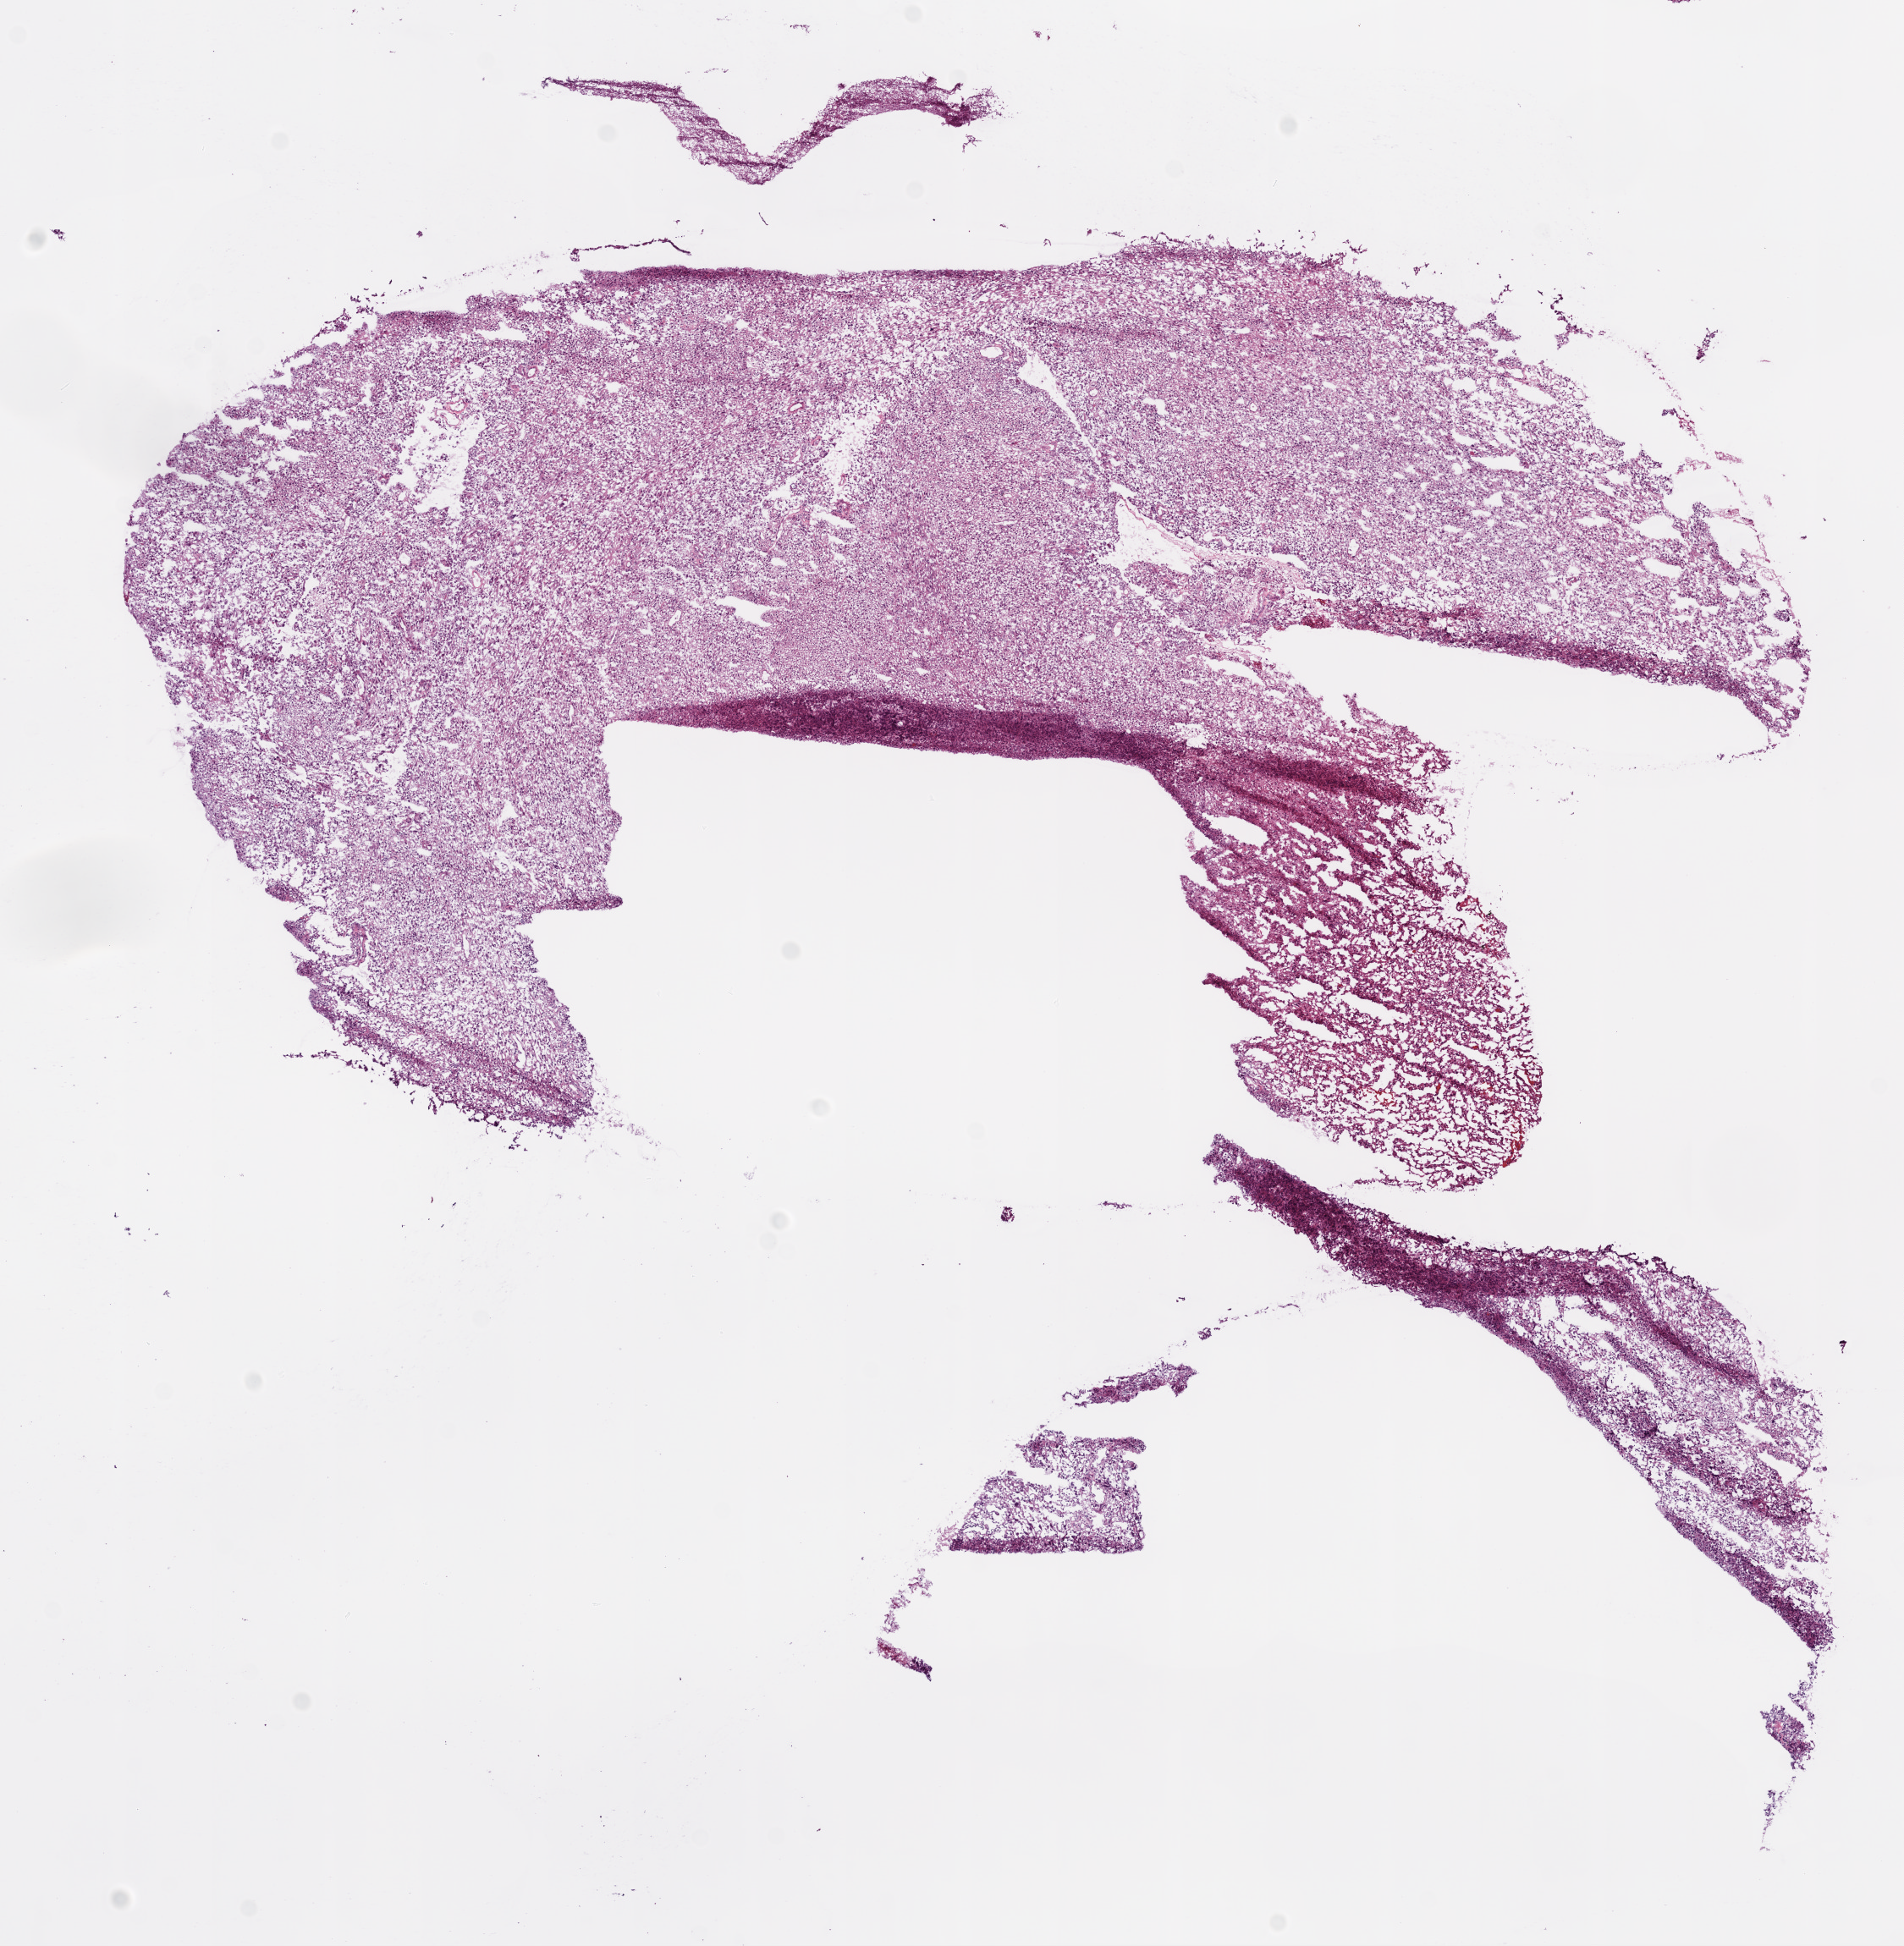
Hematoxylin and eosin (H&E) stained whole-slide image — a low-resolution overview of the entire scanned area, about 9.0 x 9.2 mm, frozen section, primary tumour sample from the brain. Male, age 60 years at initial diagnosis. Composition of this section per pathologist review: tumour cells 100%, tumour nuclei 85%, normal cells 0%, stromal cells 0%, necrosis 0%.
Diagnosis: Glioblastoma.